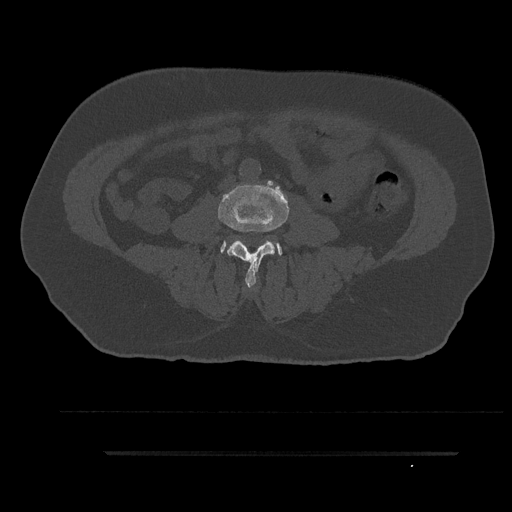
CT including the spine, one axial slice. Position 17 of 797 along the scan axis. Bone window (W 1800 / L 400 HU). 0.5 mm slice thickness. 512 × 512 image matrix, field of view 432 × 432 mm. Male patient, age 63 years. From the clinical record (not read from this slice): primary cancer: renal; vertebrae with lytic lesions (as recorded): T8.
Outlined on this slice (semi-automatic segmentation, software-assisted and operator-edited):
- L3 vertebra: bounding box [x1, y1, x2, y2] px = [218, 185, 289, 289]
- L4 vertebra: [220, 240, 282, 256]